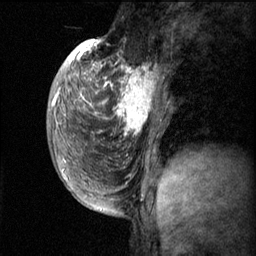
Breast MRI (dynamic contrast-enhanced), one sagittal slice. Position 20 of 60 along the scan axis. Dynamic contrast-enhanced series, image 2 of 3 at this slice position (ordered by acquisition). 1.5 T. TE 4.2 ms, TR 11.1 ms. 256 × 256 image matrix, field of view 180 × 180 mm. Female patient, age 50 years.
Annotated regions visible in this slice (semi-automatic segmentation, software-assisted and operator-edited):
- analysis volume of interest (the breast-tissue region the enhancement analysis was run in; not a lesion): box from (x=82, y=56) to (x=168, y=143) px
- tumour enhancement mask (voxels above the 70 % enhancement threshold inside the analysis volume of interest): (x=82, y=62)–(x=159, y=135)